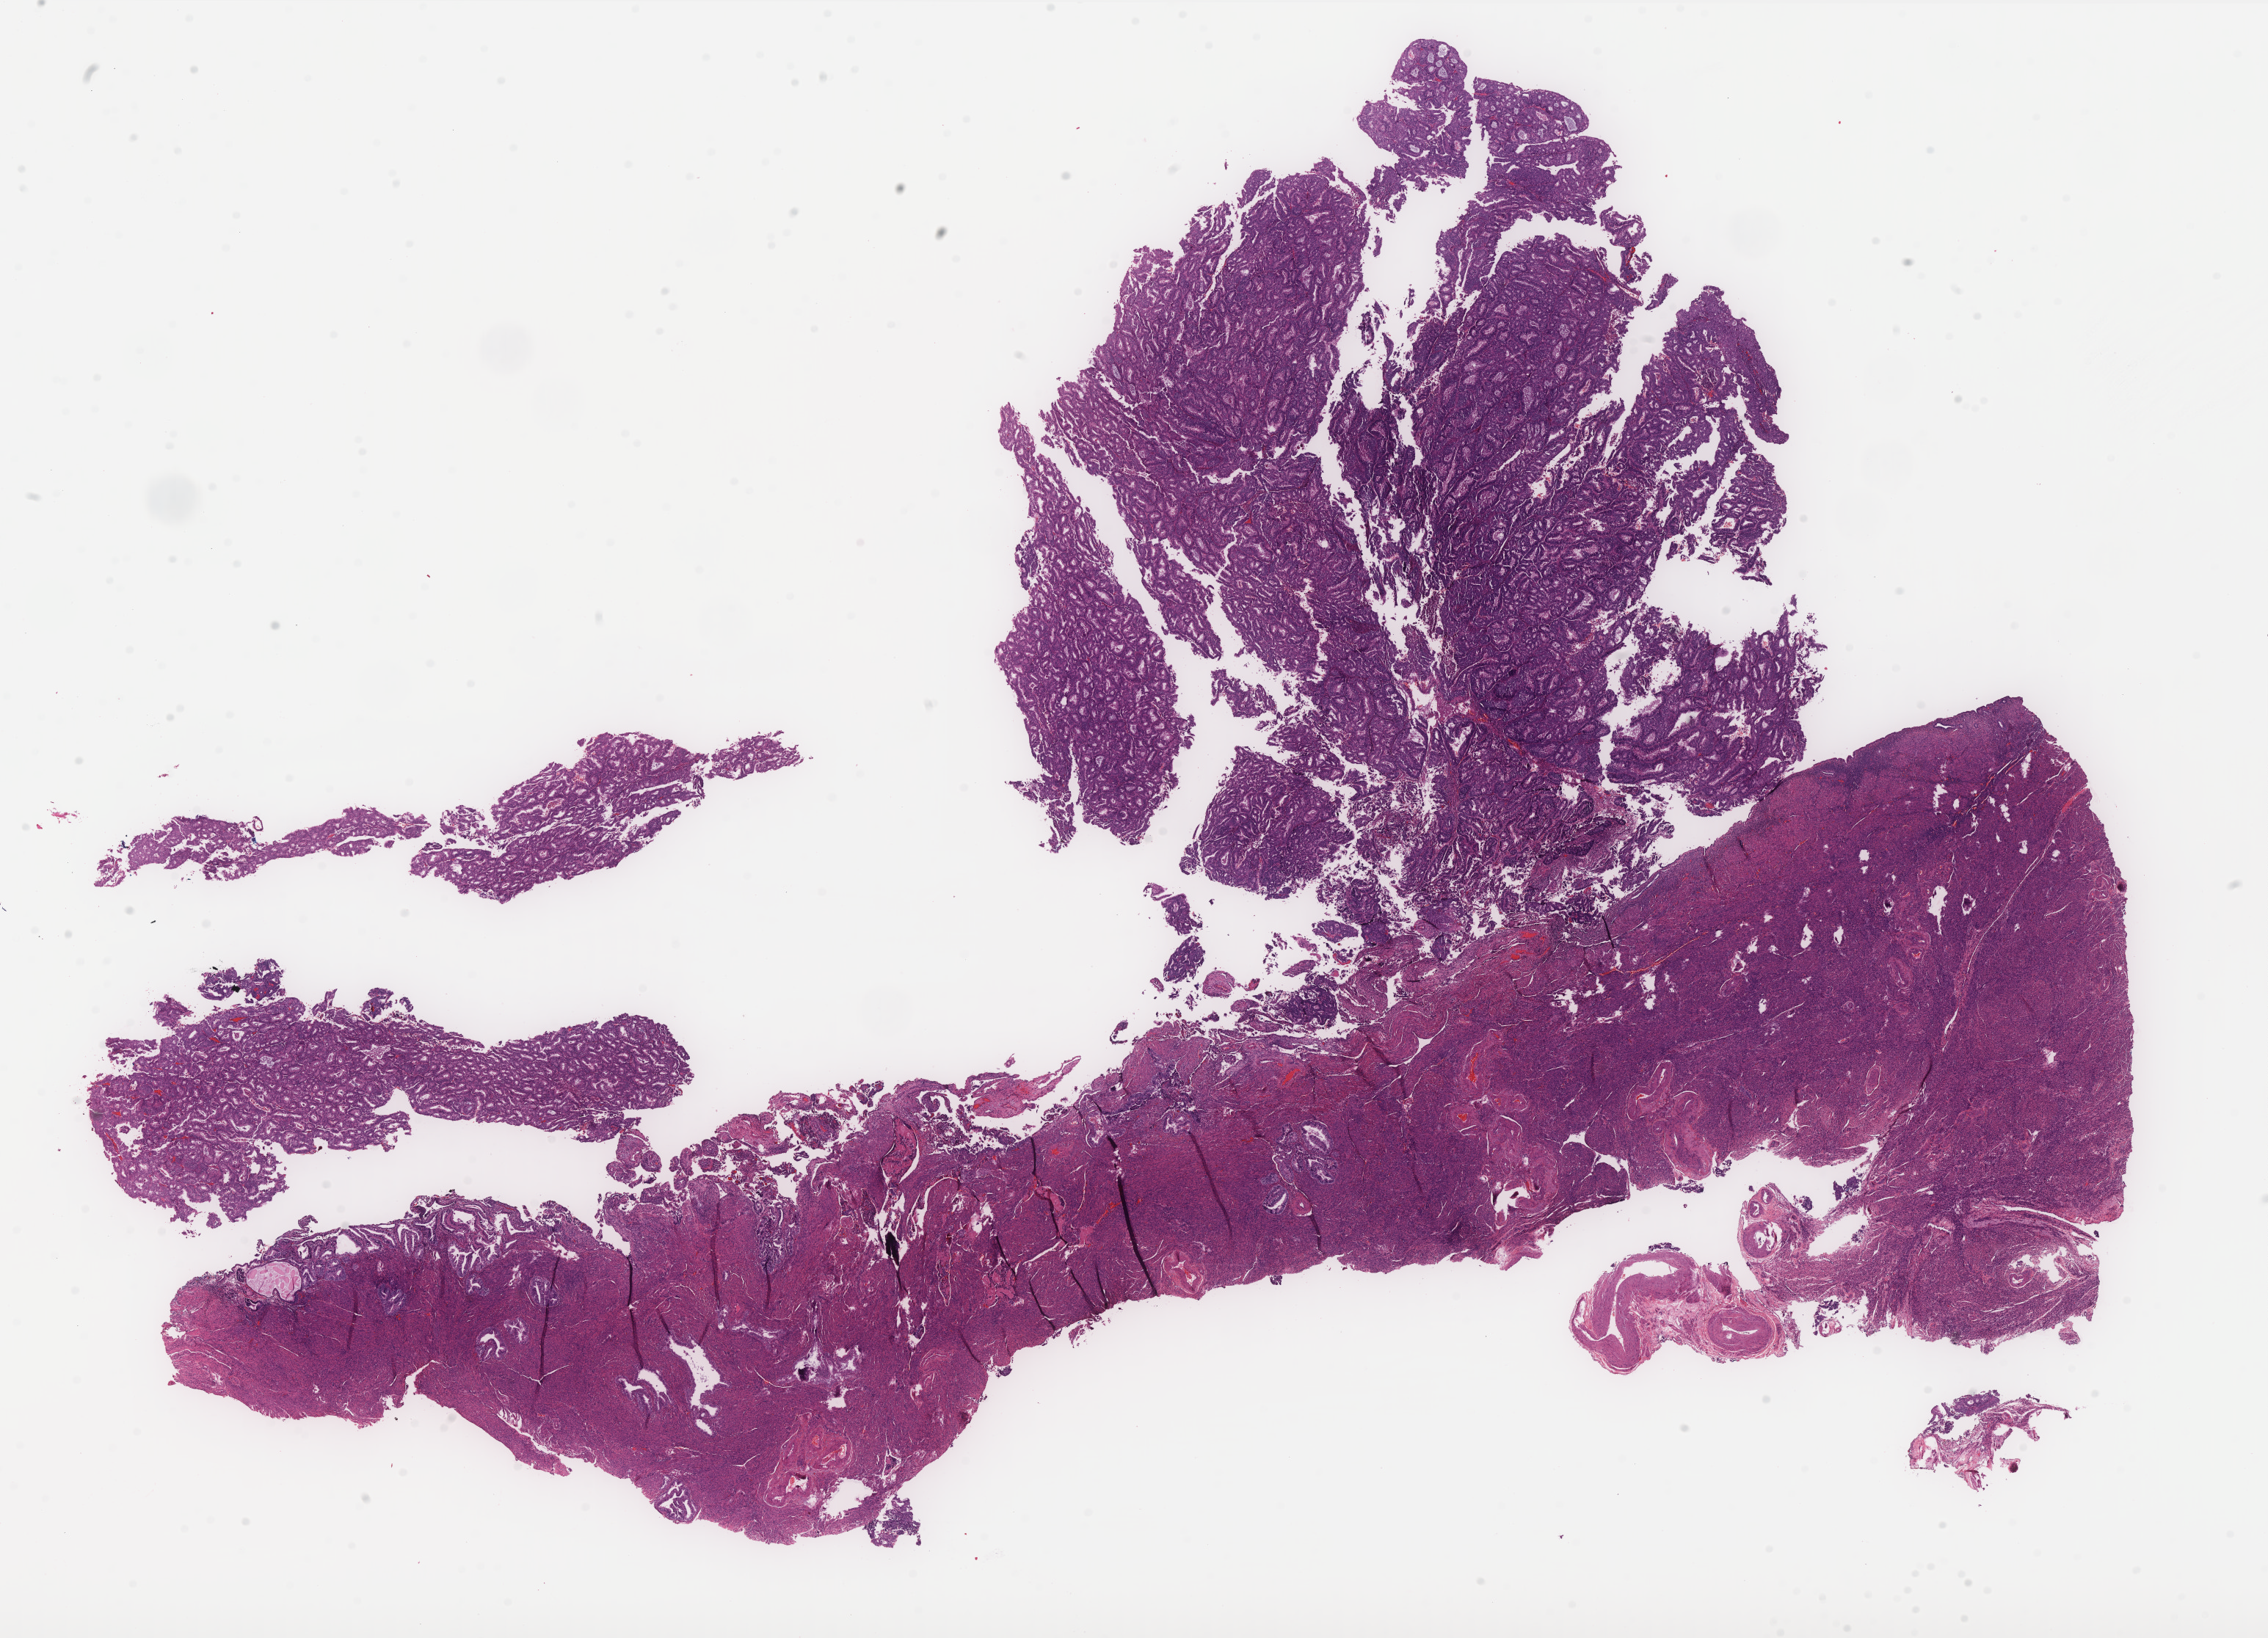
Whole-slide histology image, Hematoxylin and eosin (H&E) stained — low-resolution overview of the scanned area, about 24.8 x 17.9 mm. Formalin-fixed paraffin-embedded (FFPE) diagnostic section. Uterus, primary tumour sample. Female, age 67 years at initial diagnosis. Histologic grade: G1 (well differentiated).
Histologic diagnosis: Endometrioid adenocarcinoma, NOS. FIGO stage: IA.